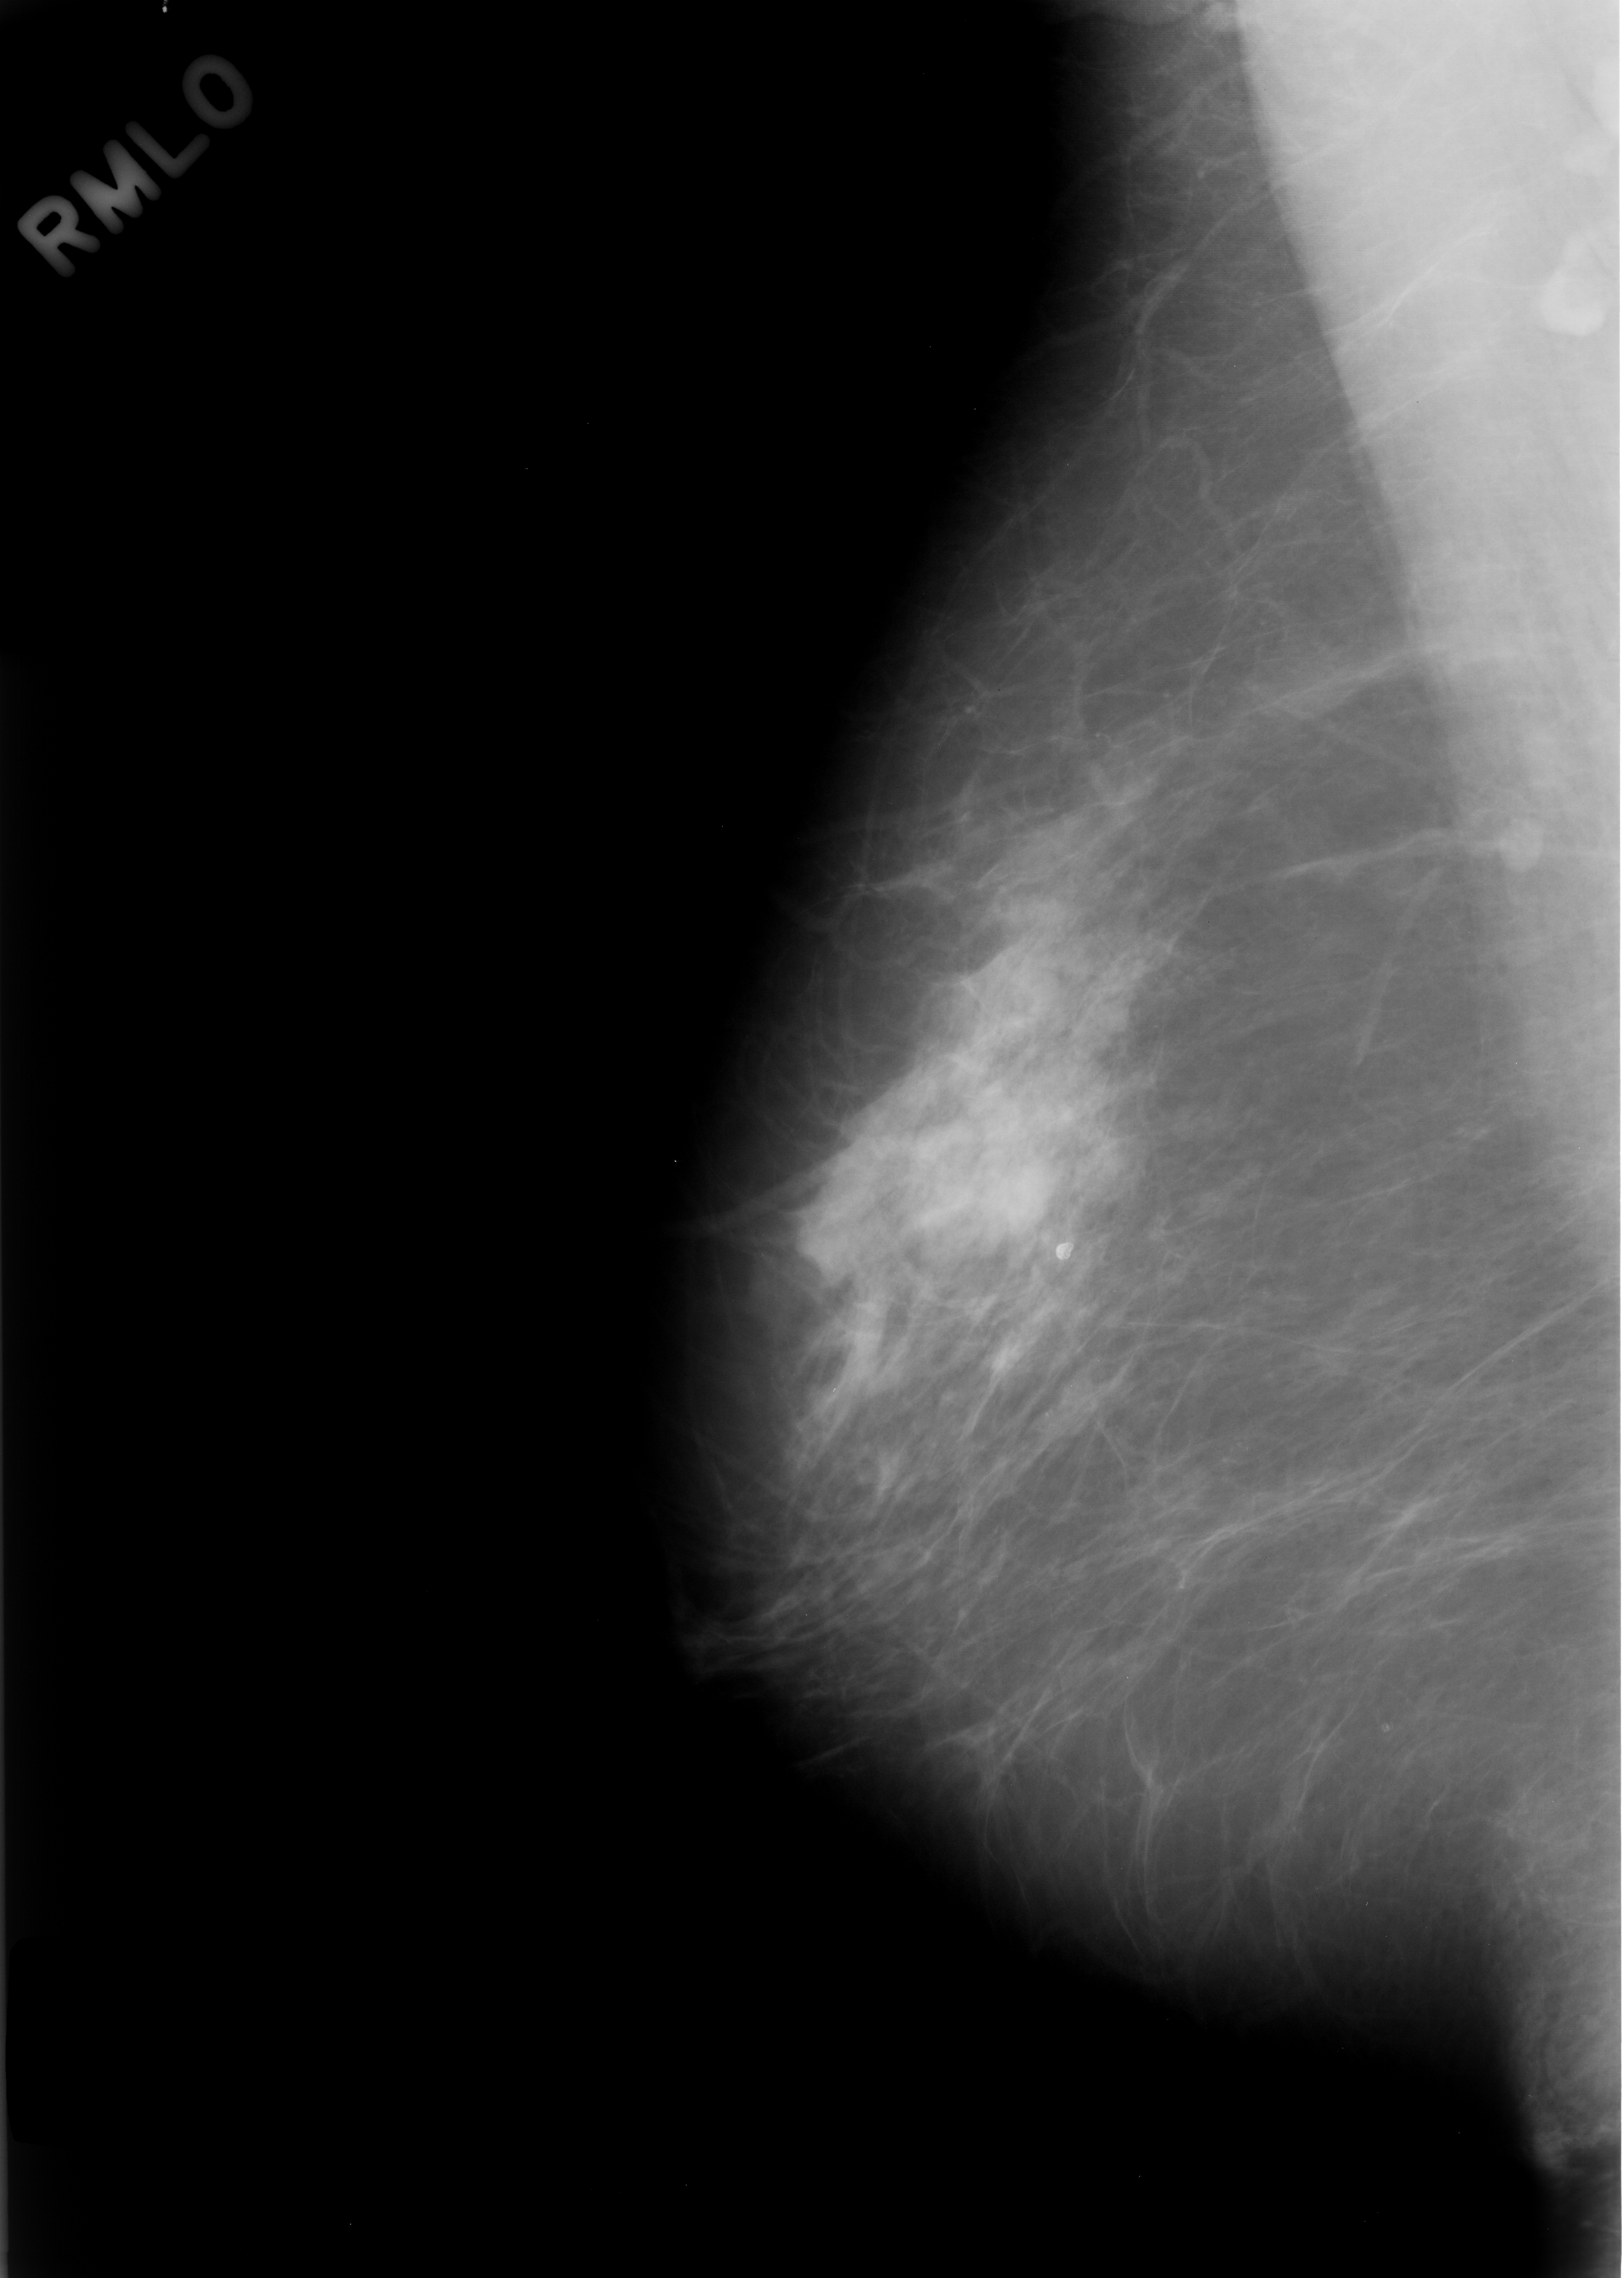
Digitized screen-film mammogram; right breast; mediolateral oblique (MLO) view; BI-RADS breast density category 2 (scale 1–4); 1624 × 2278 image matrix.
Marked abnormalities (boxes around the expert regions of interest):
- mass, shape lobulated, margins microlobulated; BI-RADS assessment category 3; outcome (as recorded, no biopsy): benign without callback (not worked up further): bounding box <916,1078,1069,1249> (left, top, right, bottom; pixels)